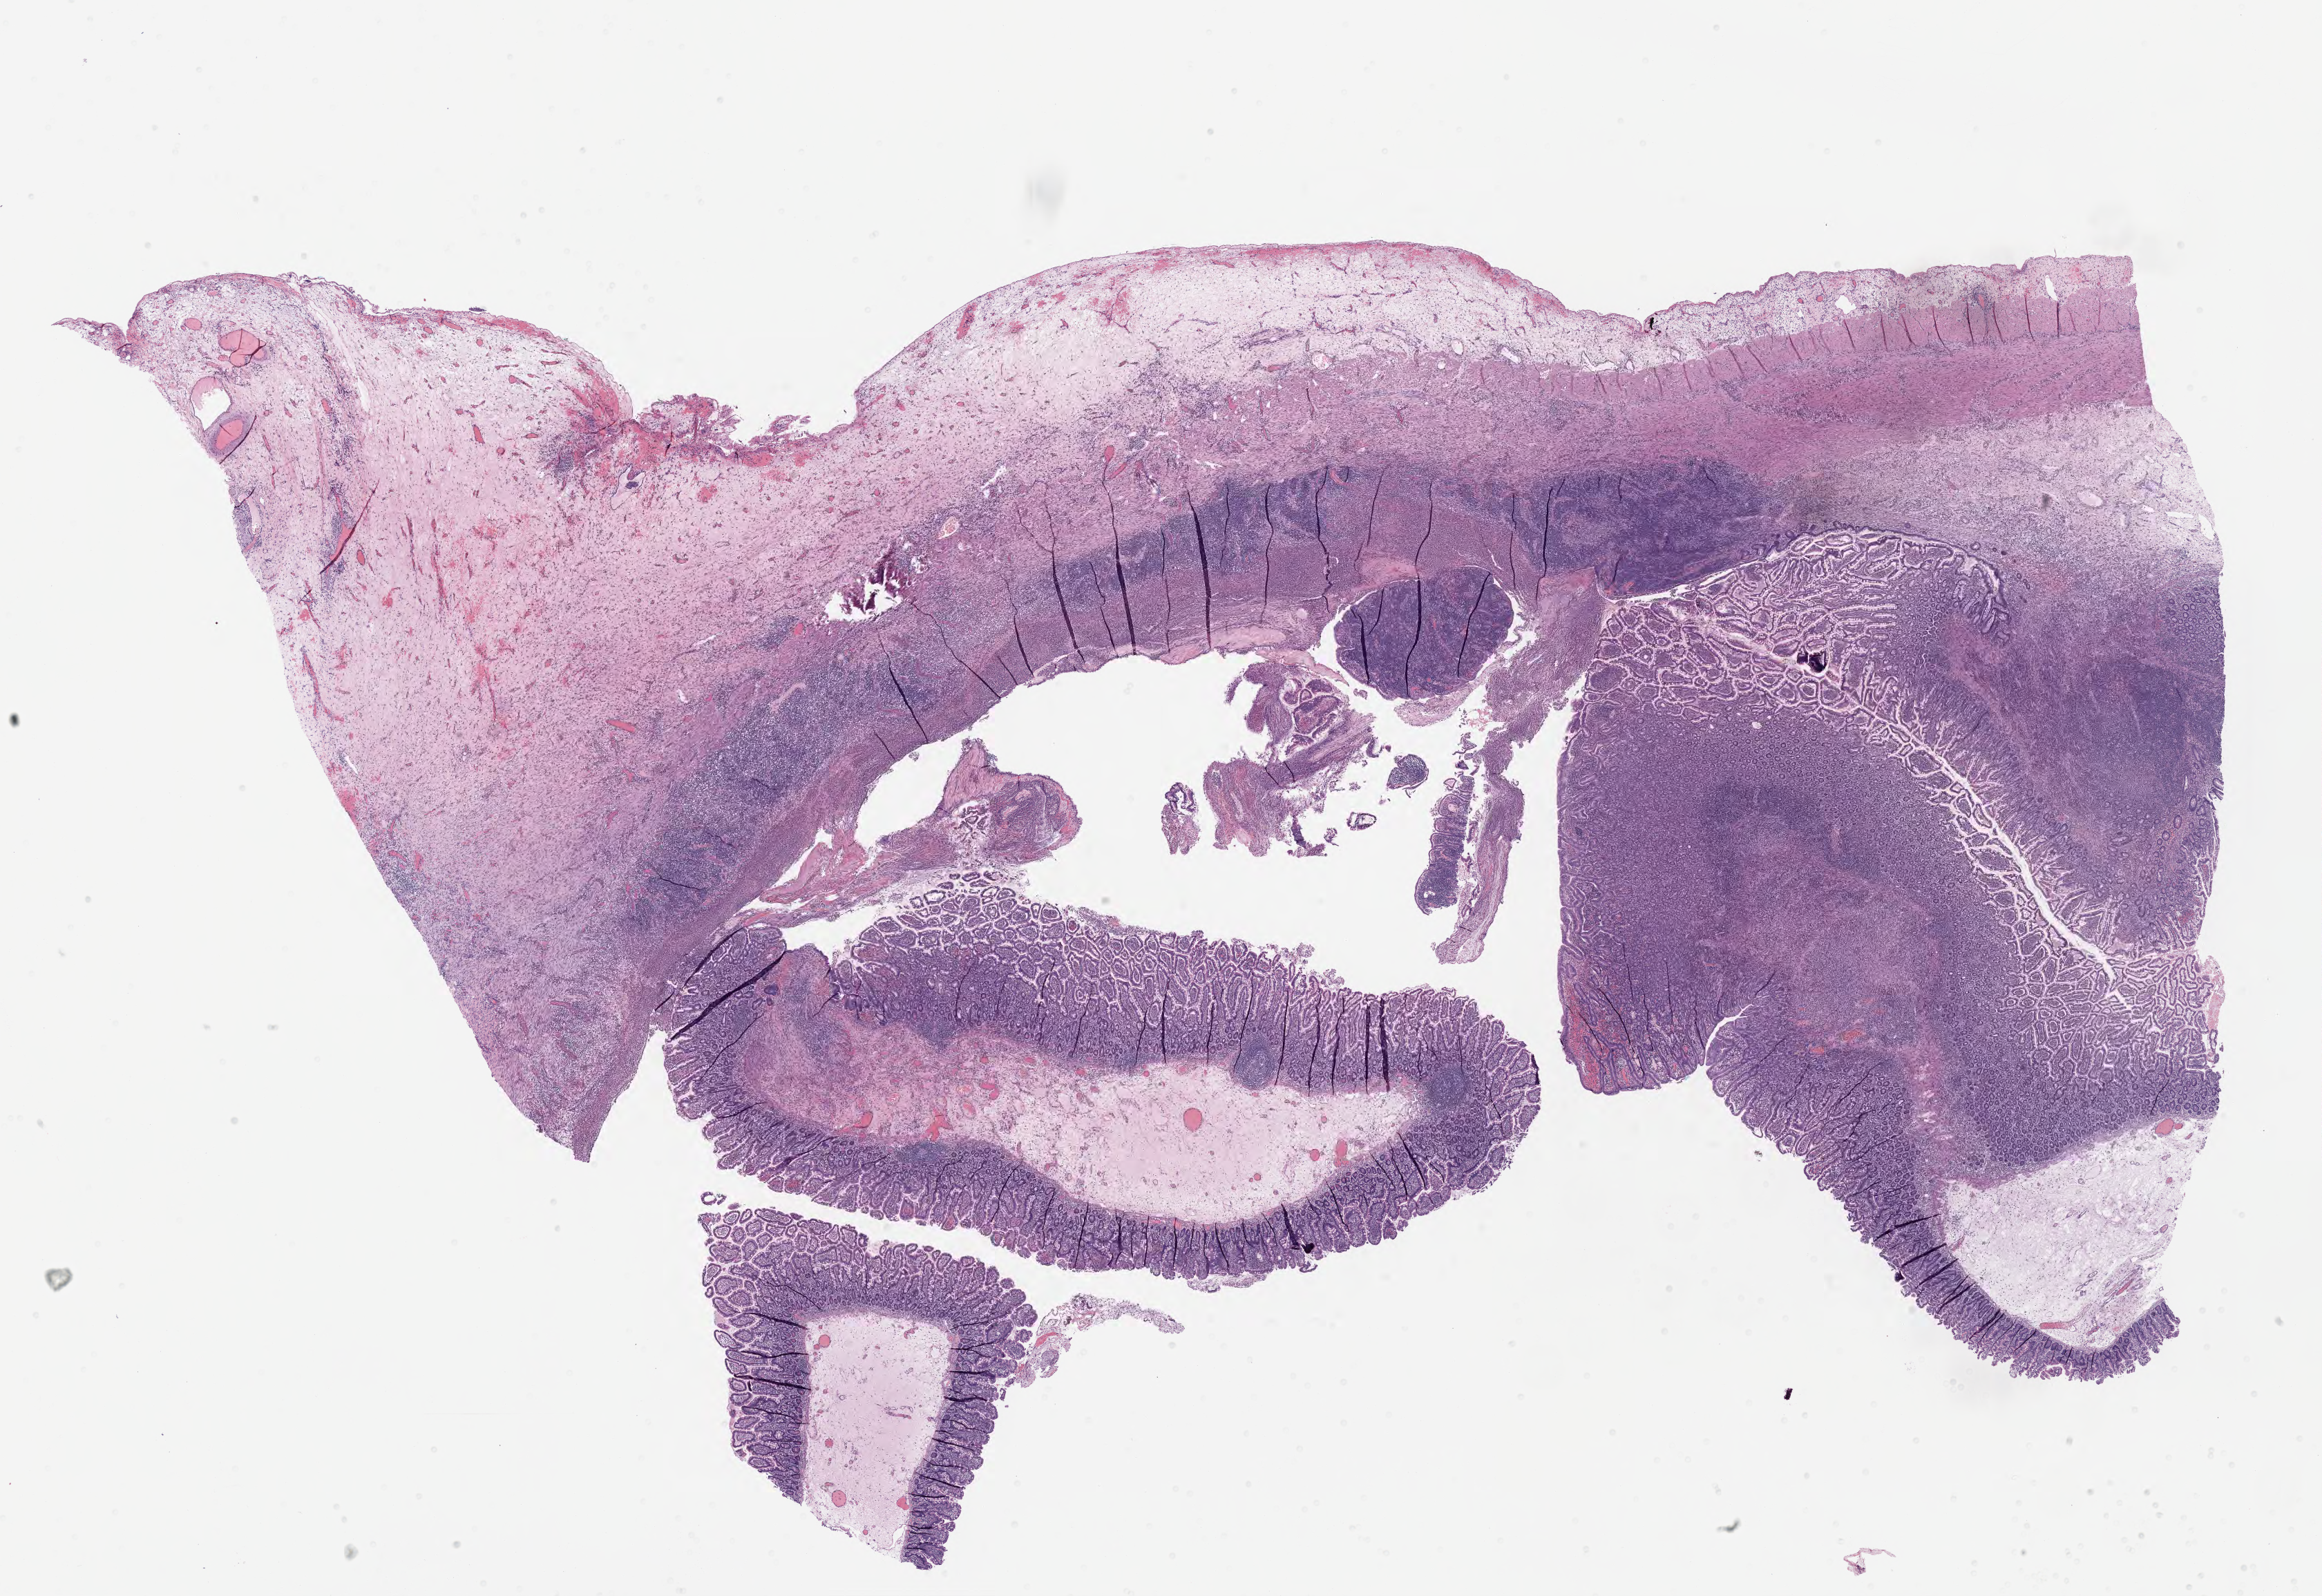
Hematoxylin and eosin (H&E) whole-slide image, shown as a low-resolution overview of the whole scanned area (about 27.2 x 18.7 mm); tumor tissue. Patient female; aged 44.
- histologic diagnosis: Burkitt lymphoma, NOS